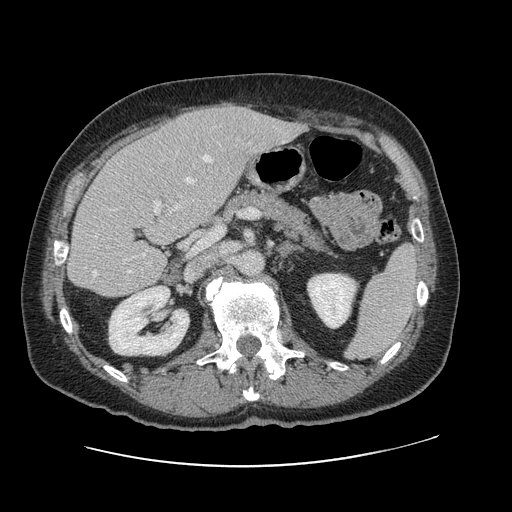
Contrast-enhanced abdominal CT, one axial slice. Slice 56 of 138 in the series (ordered by position). 120 kVp. Intravenous contrast given. Soft-tissue window (W 400 / L 40 HU). 2.5 mm slice thickness. 512 × 512 image matrix, field of view 402 × 402 mm. Male patient, age 71 years. From the clinical record (not read from this slice): diagnosis: colorectal cancer liver metastases, imaged before liver resection; multiple liver metastases: no; largest metastasis: 3.3 cm.
Outlined on this slice (manually delineated by an expert):
- hepatic veins: bounding box [x1, y1, x2, y2] px = [93, 155, 227, 277]
- liver: [70, 105, 302, 296]
- planned liver remnant (the part of the liver to remain after resection): [70, 143, 201, 296]
- portal vein (with intrahepatic branches): [154, 201, 181, 213]